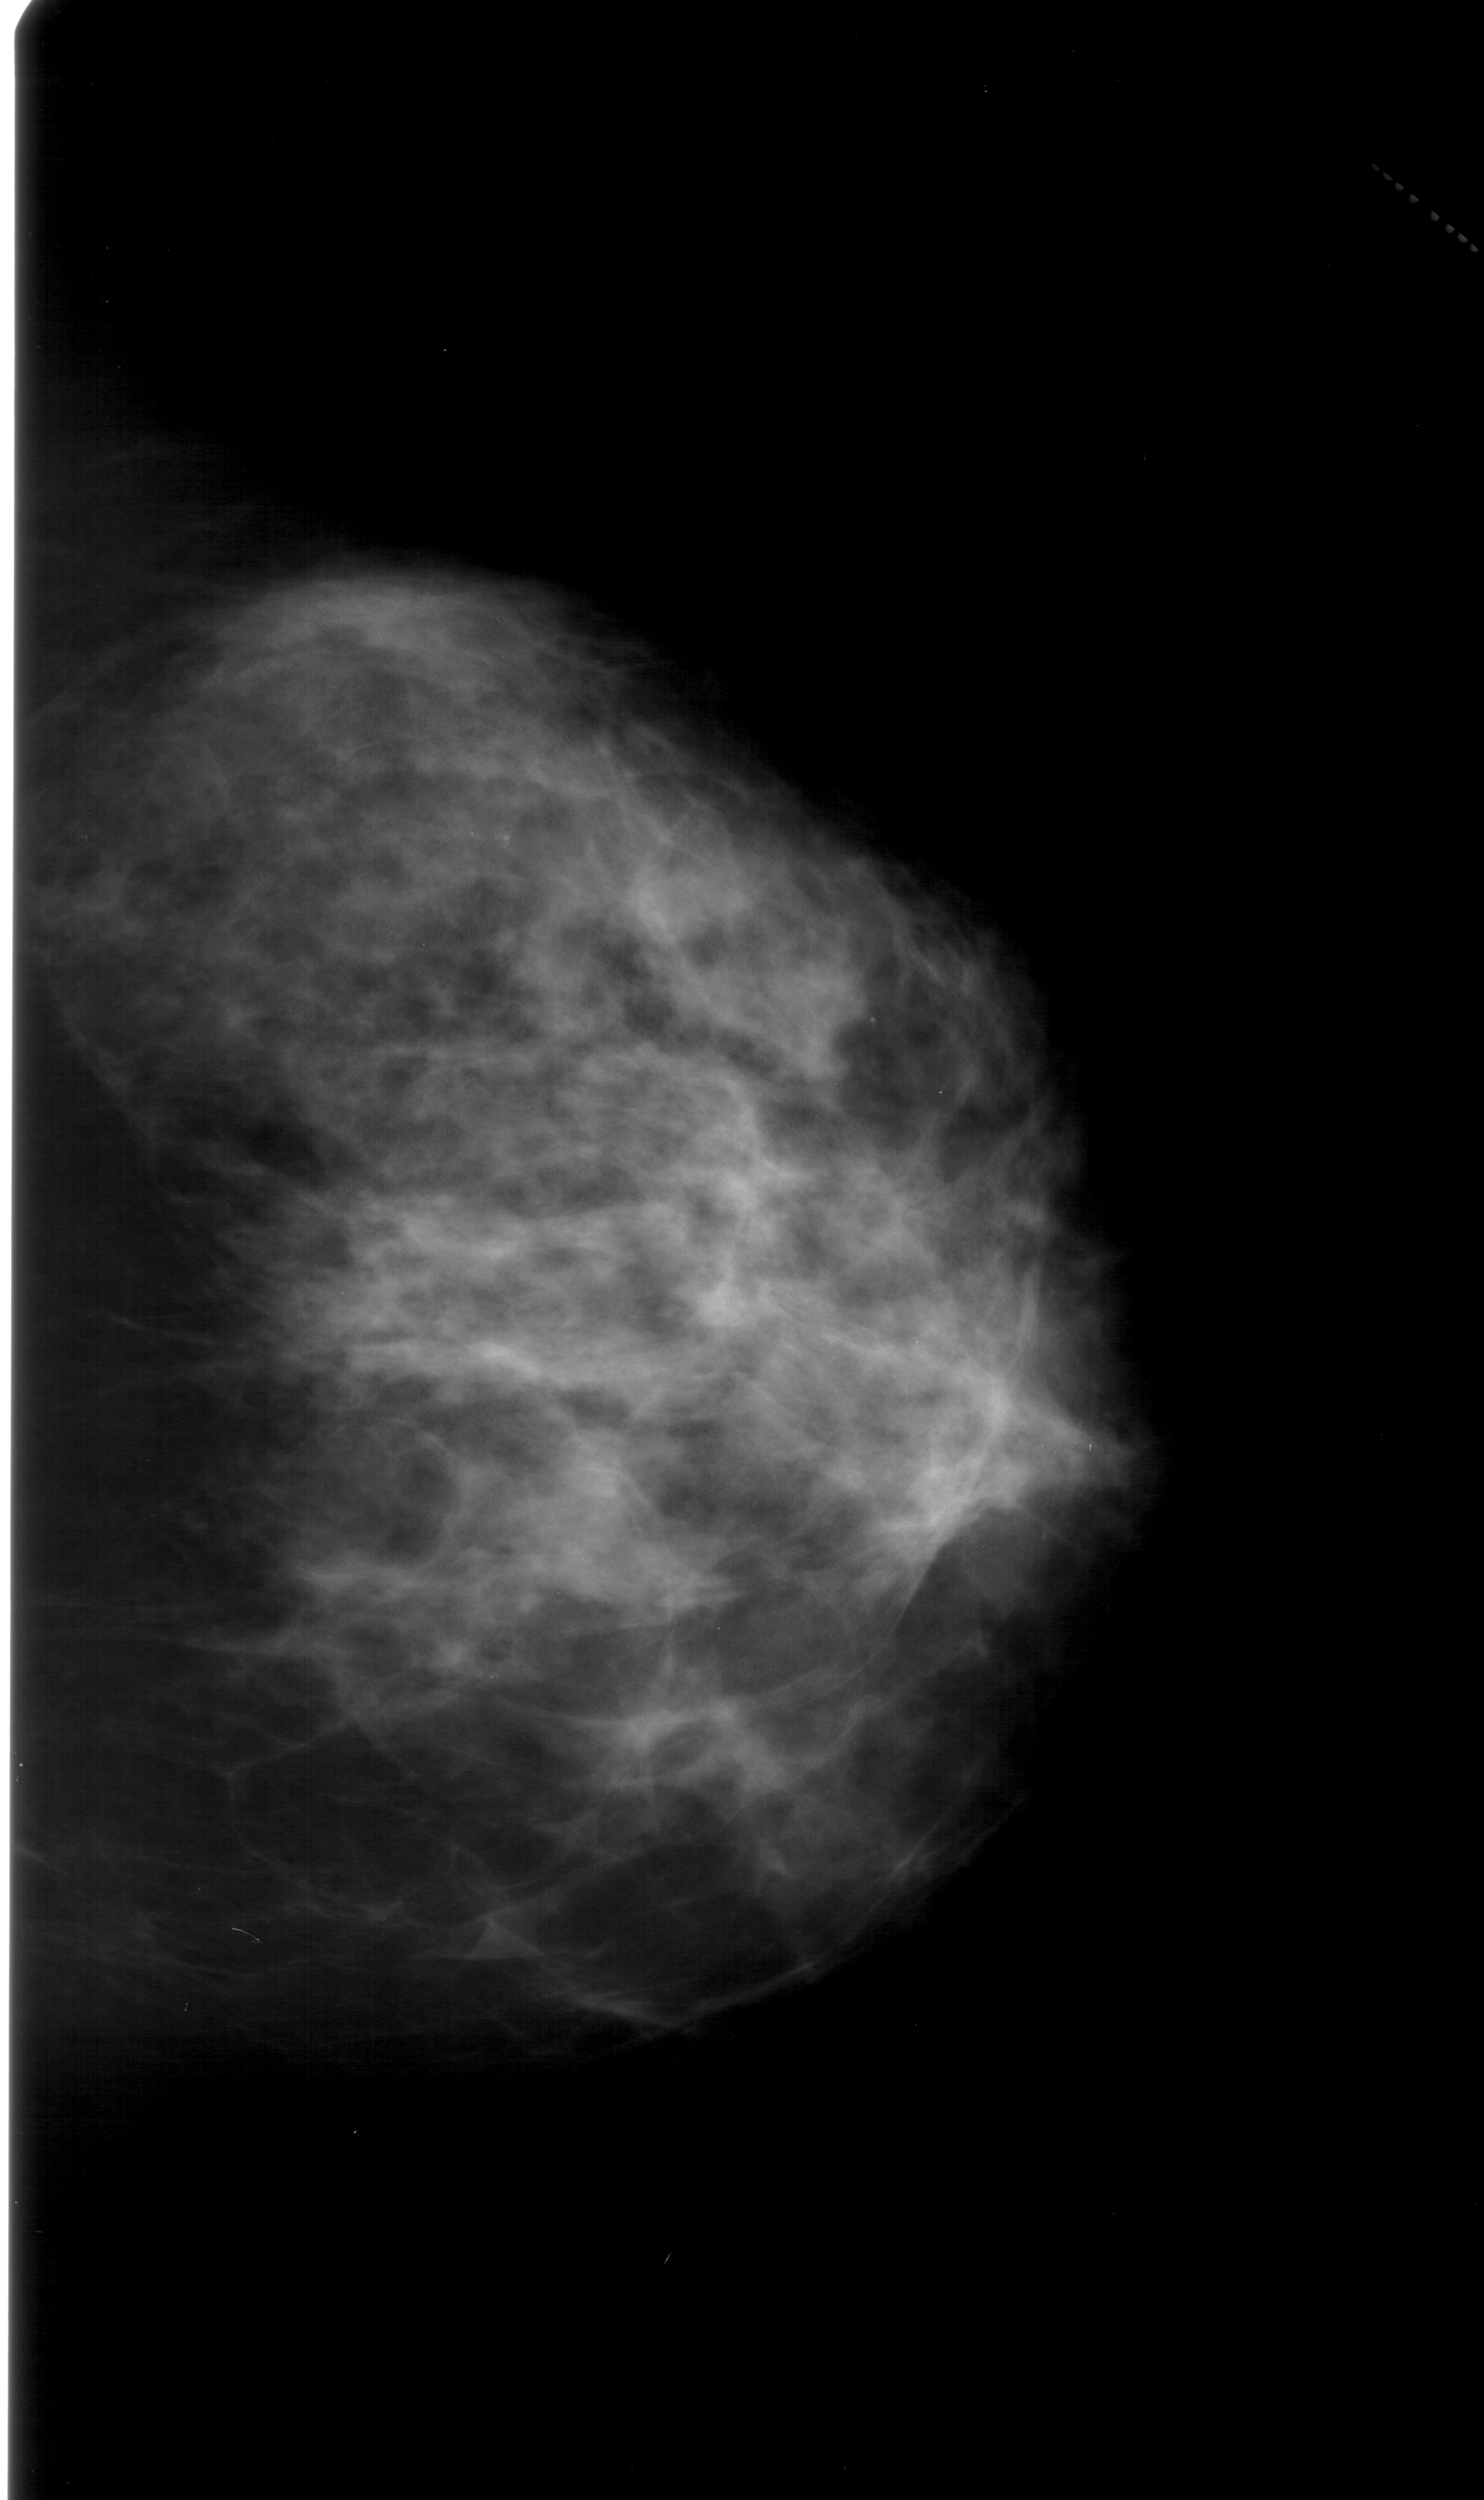
Digitized screen-film mammogram; right breast; craniocaudal (CC) view; breast composition: heterogeneously dense (BI-RADS density category 3 of 4).
Finding: calcifications, morphology pleomorphic, distribution clustered; BI-RADS assessment category 4; pathology result (as recorded, not read from the image): benign.